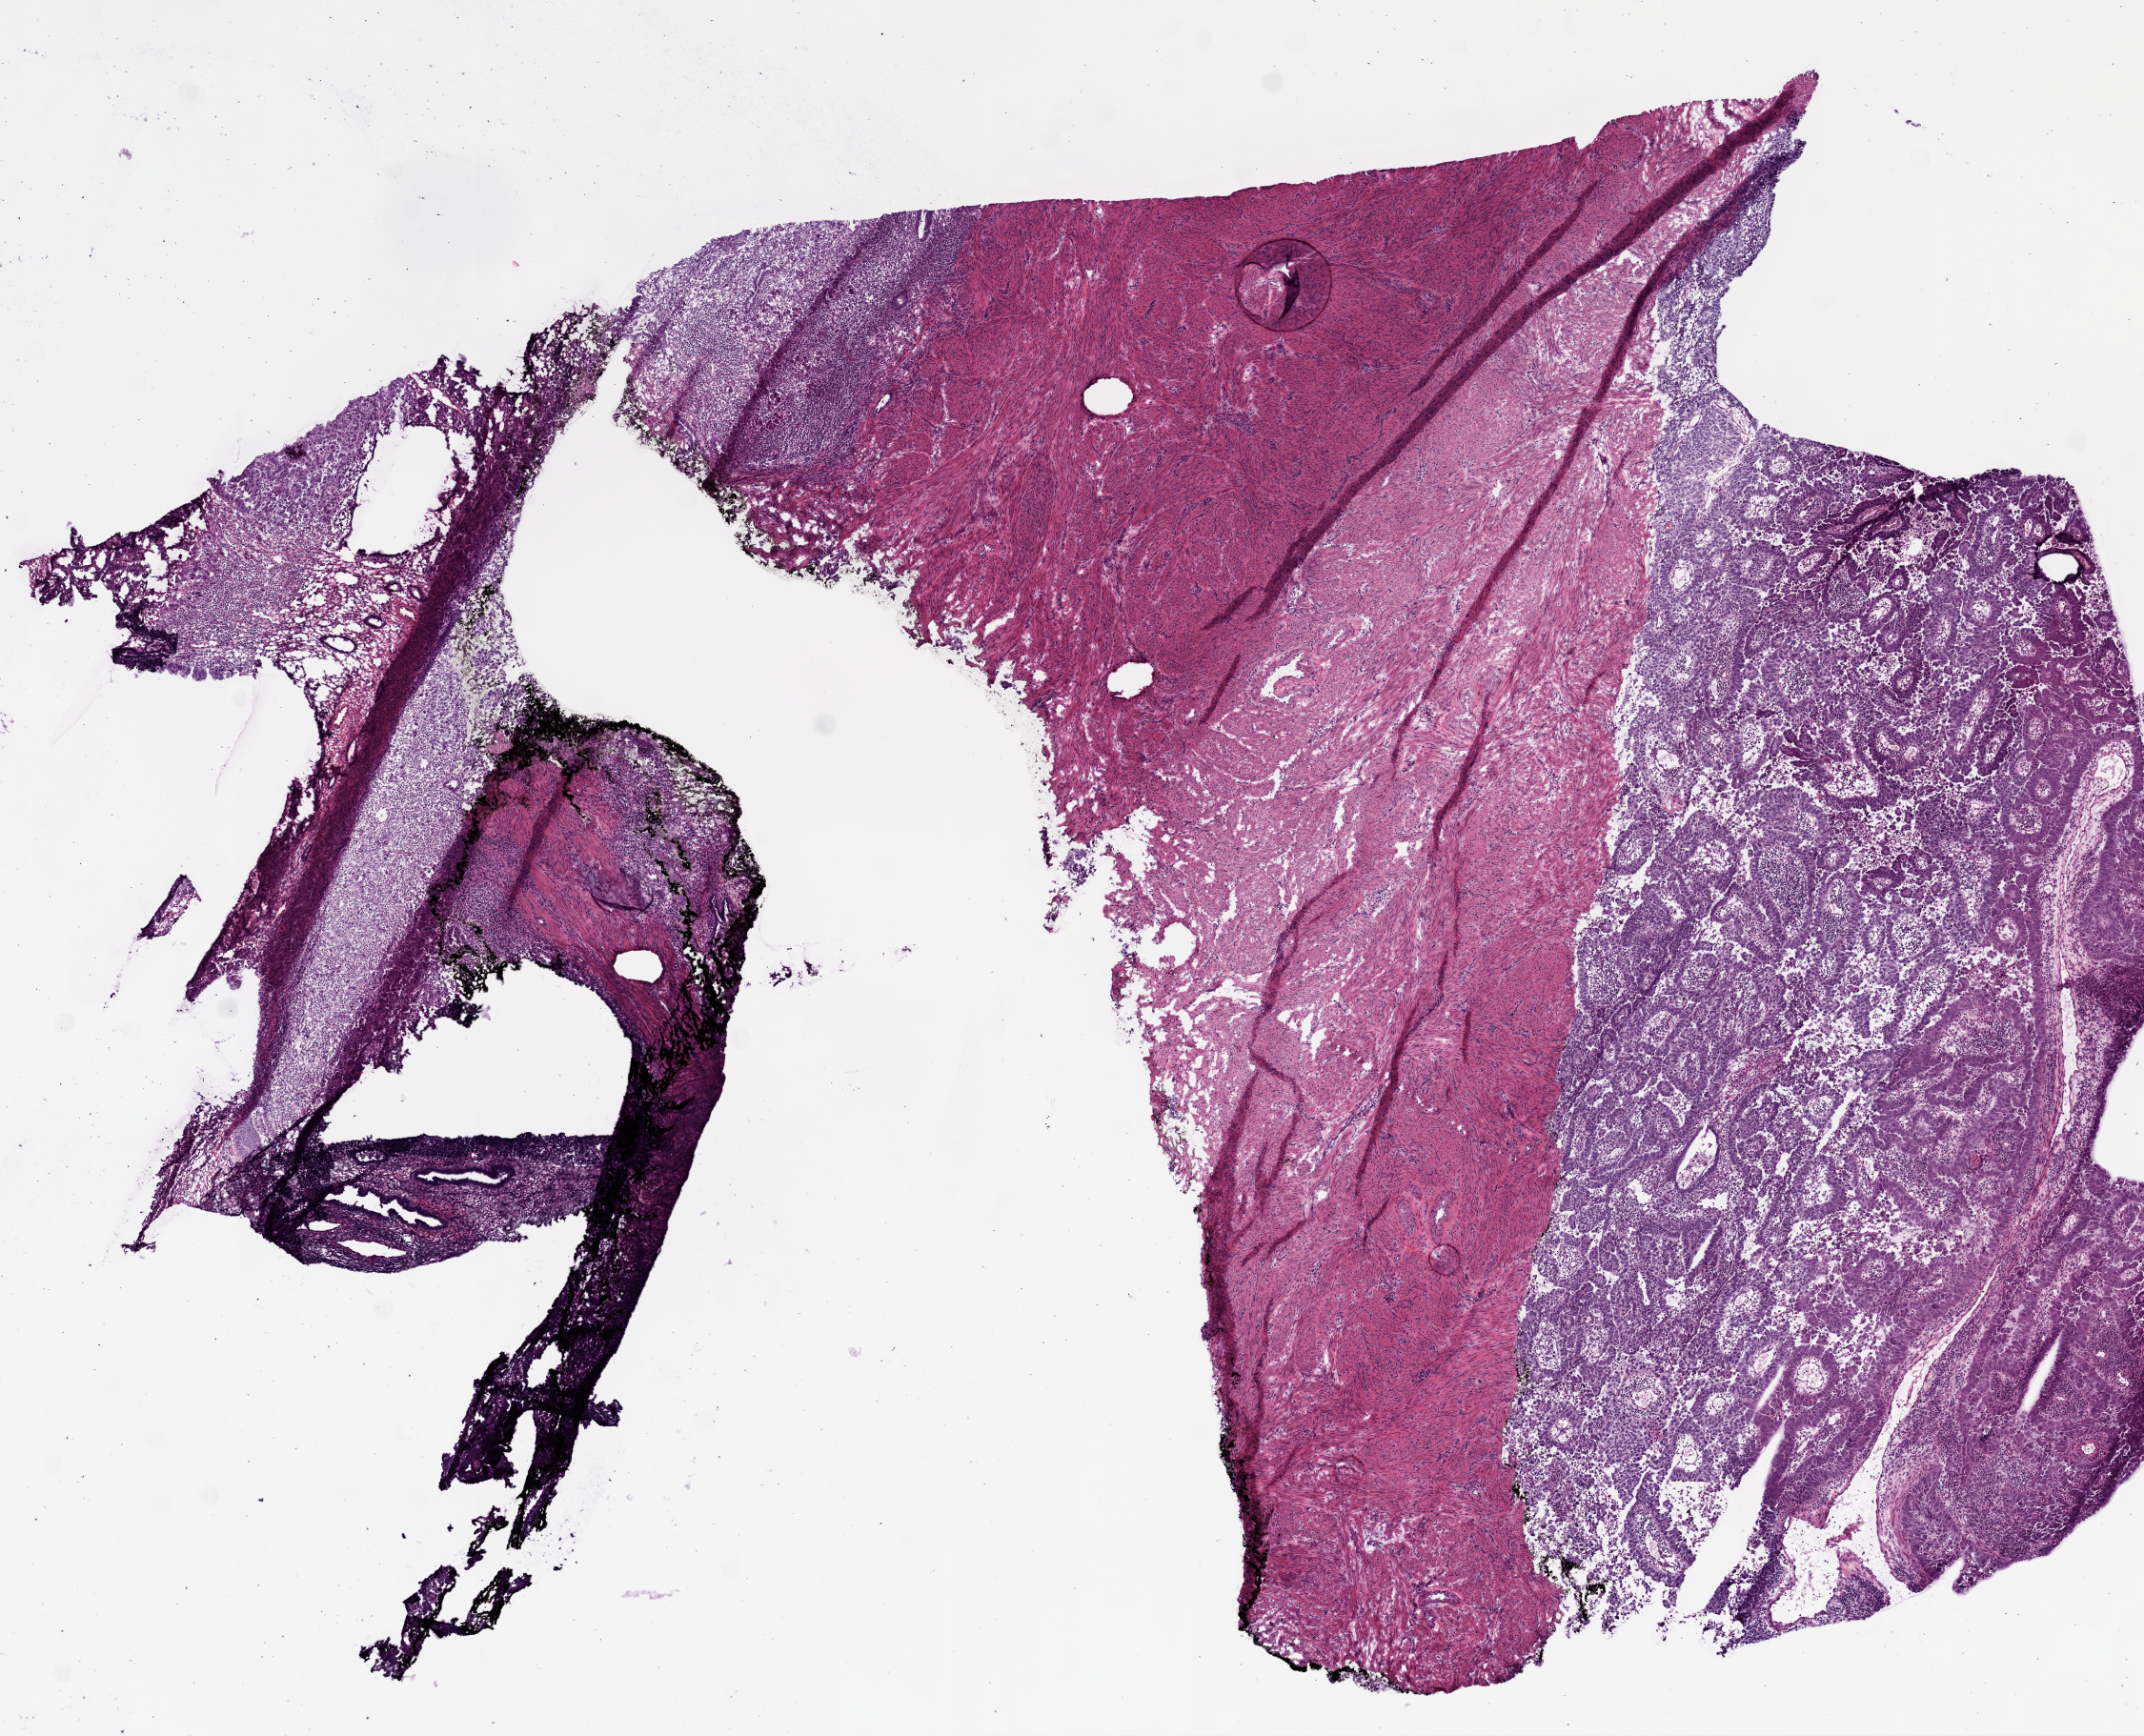
H&E-stained whole-slide image — shown as a low-resolution overview of the whole scanned area (about 9.0 x 7.3 mm, from a 20x scan). Frozen section. Primary tumour sample from the uterus. Patient: female, age at initial diagnosis 57 years. Histologic grade: G3 (poorly differentiated). Composition of this section per pathologist review: tumour cells 40%, tumour nuclei 40%, normal cells 0%, stromal cells 60%, necrosis 0%. Inflammatory infiltration, as recorded: lymphocyte infiltration 0%, monocyte infiltration 0%, neutrophil infiltration 0%.
FIGO stage: IIIA. Histologic diagnosis: Serous cystadenocarcinoma, NOS (endometrium).